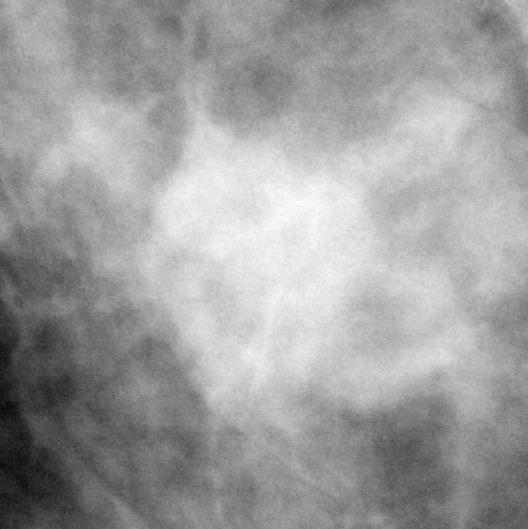
Crop from a digitized film mammogram around one marked abnormality; right breast; CC view; BI-RADS breast density category 2 (scale 1–4).
Mass, shape oval, margins ill defined; BI-RADS assessment category 4; pathology result (as recorded, not read from the image): benign.